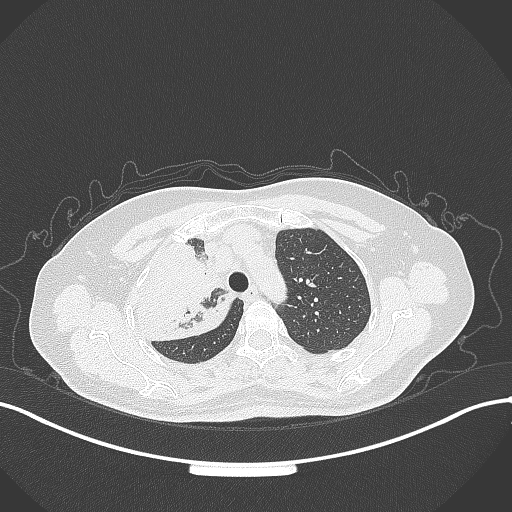
Chest CT, one axial slice; position 245 of 309 along the scan axis; reconstruction kernel B70f; lung window (W 1500 / L -600 HU); 1 mm slice thickness; 512 × 512 image matrix, field of view 400 × 400 mm. Female patient, age 60 years. Case-level facts recorded for this patient, not image findings: clinical TNM (as recorded): T3 N1 M1.
Outlined on this slice (rectangle marked by the reading radiologist):
- lung tumour (recorded histology: adenocarcinoma): box from (x=130, y=229) to (x=234, y=350) px